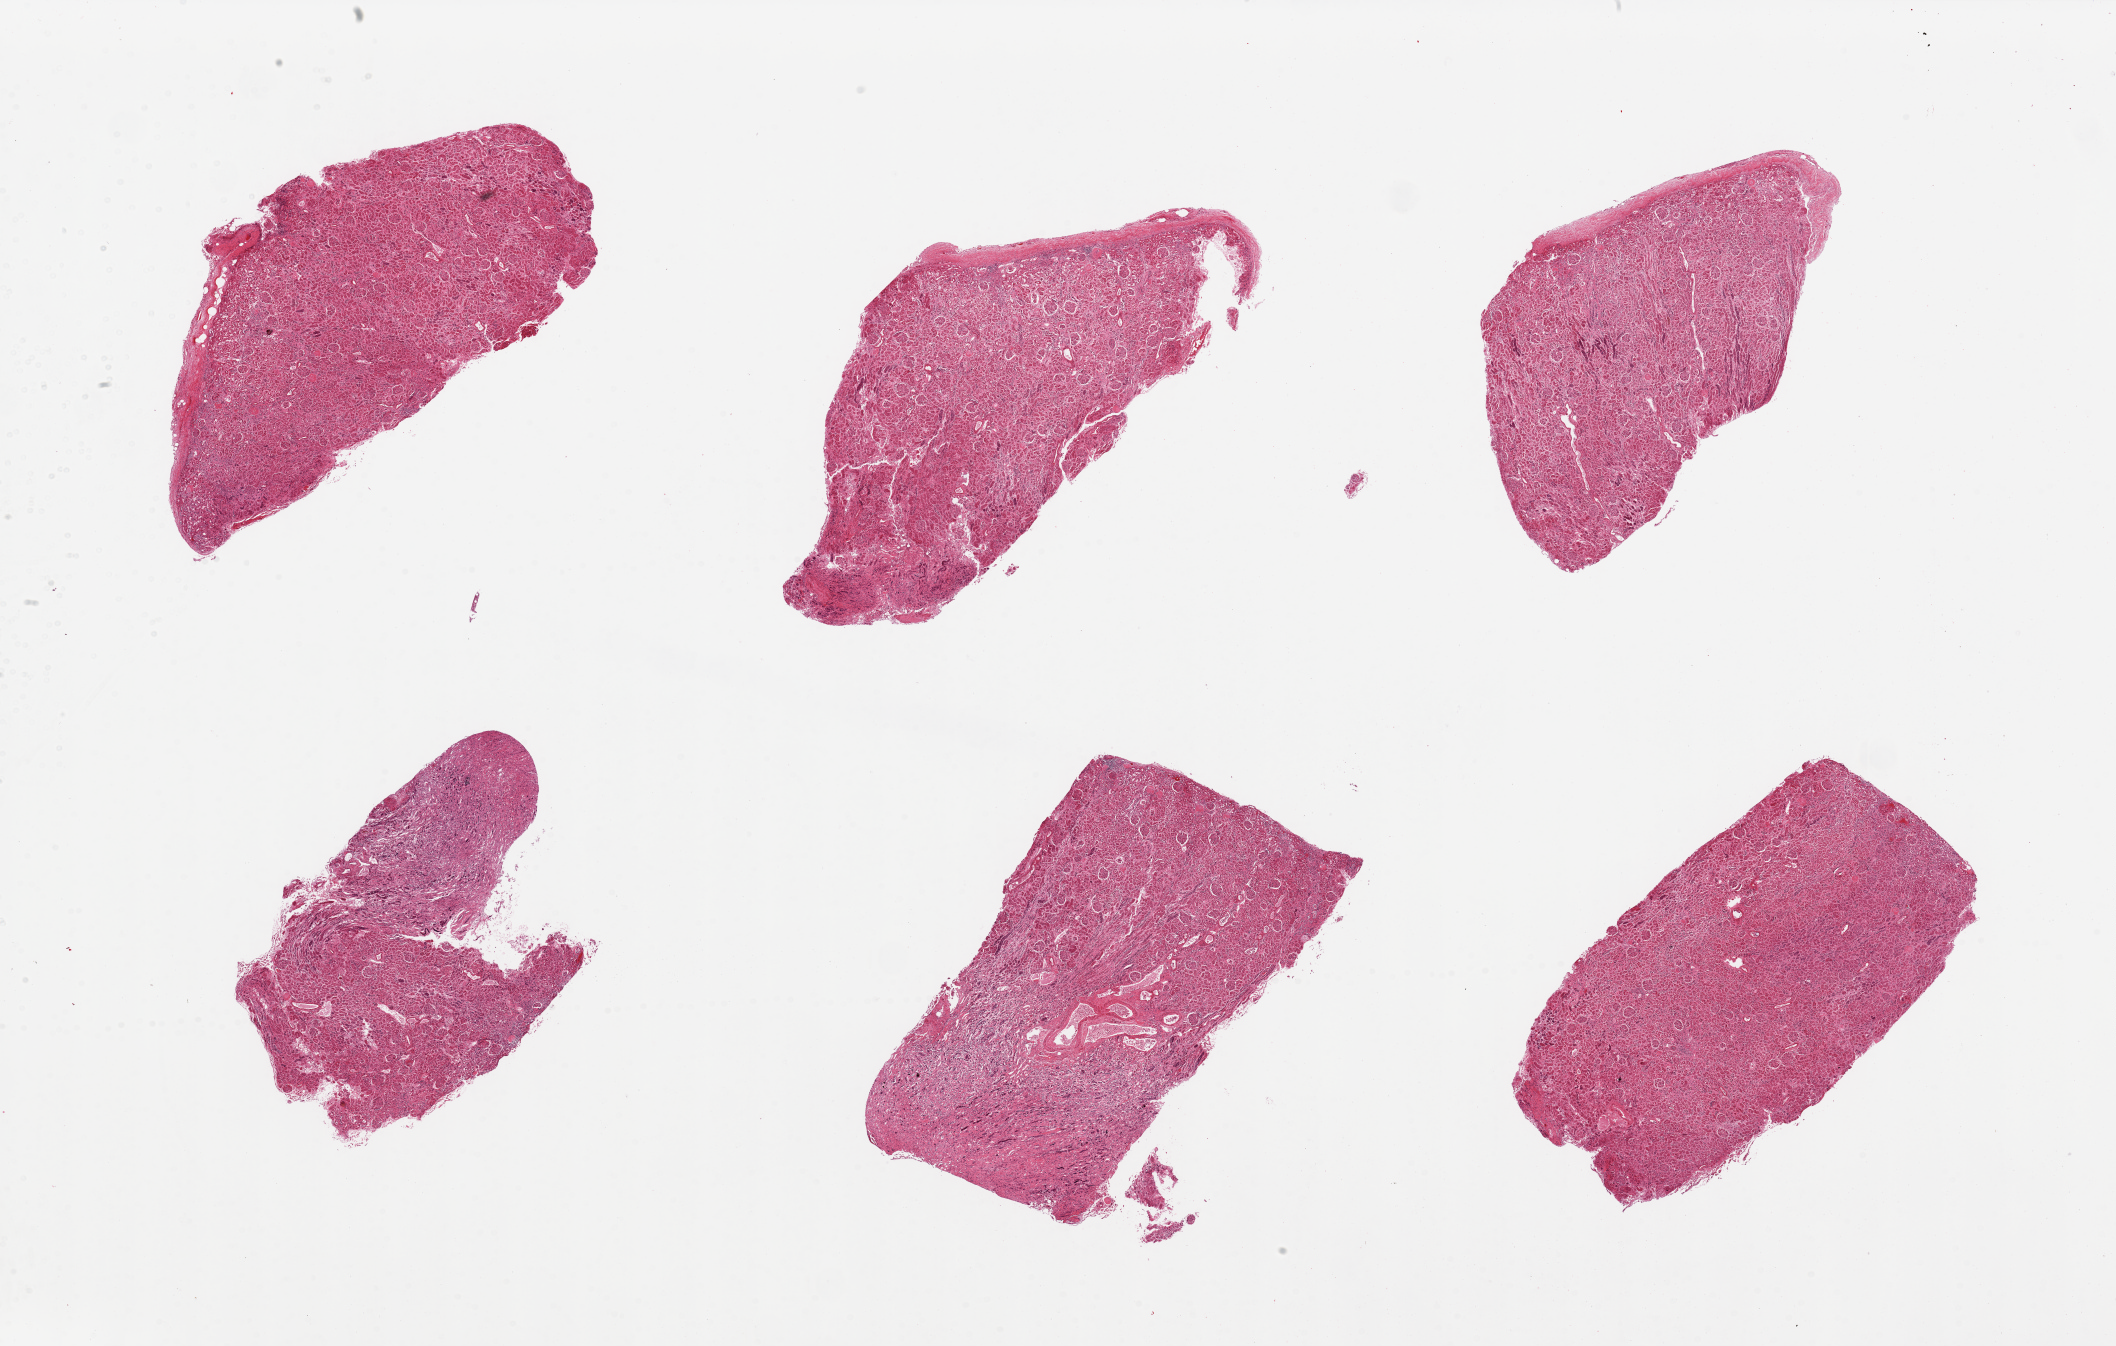
Hematoxylin and eosin (H&E) whole-slide image, low-resolution overview of the scanned area, about 33.5 x 21.3 mm (slide scanned at 20x); PAXgene-fixed paraffin-embedded (PFPE) section; target tissue: renal cortex; tissue donor sample. Female donor.
• review note (as recorded): 6 pieces, all with glomeruli; 2/6 sections are ~50% medulla; badly autolyzed